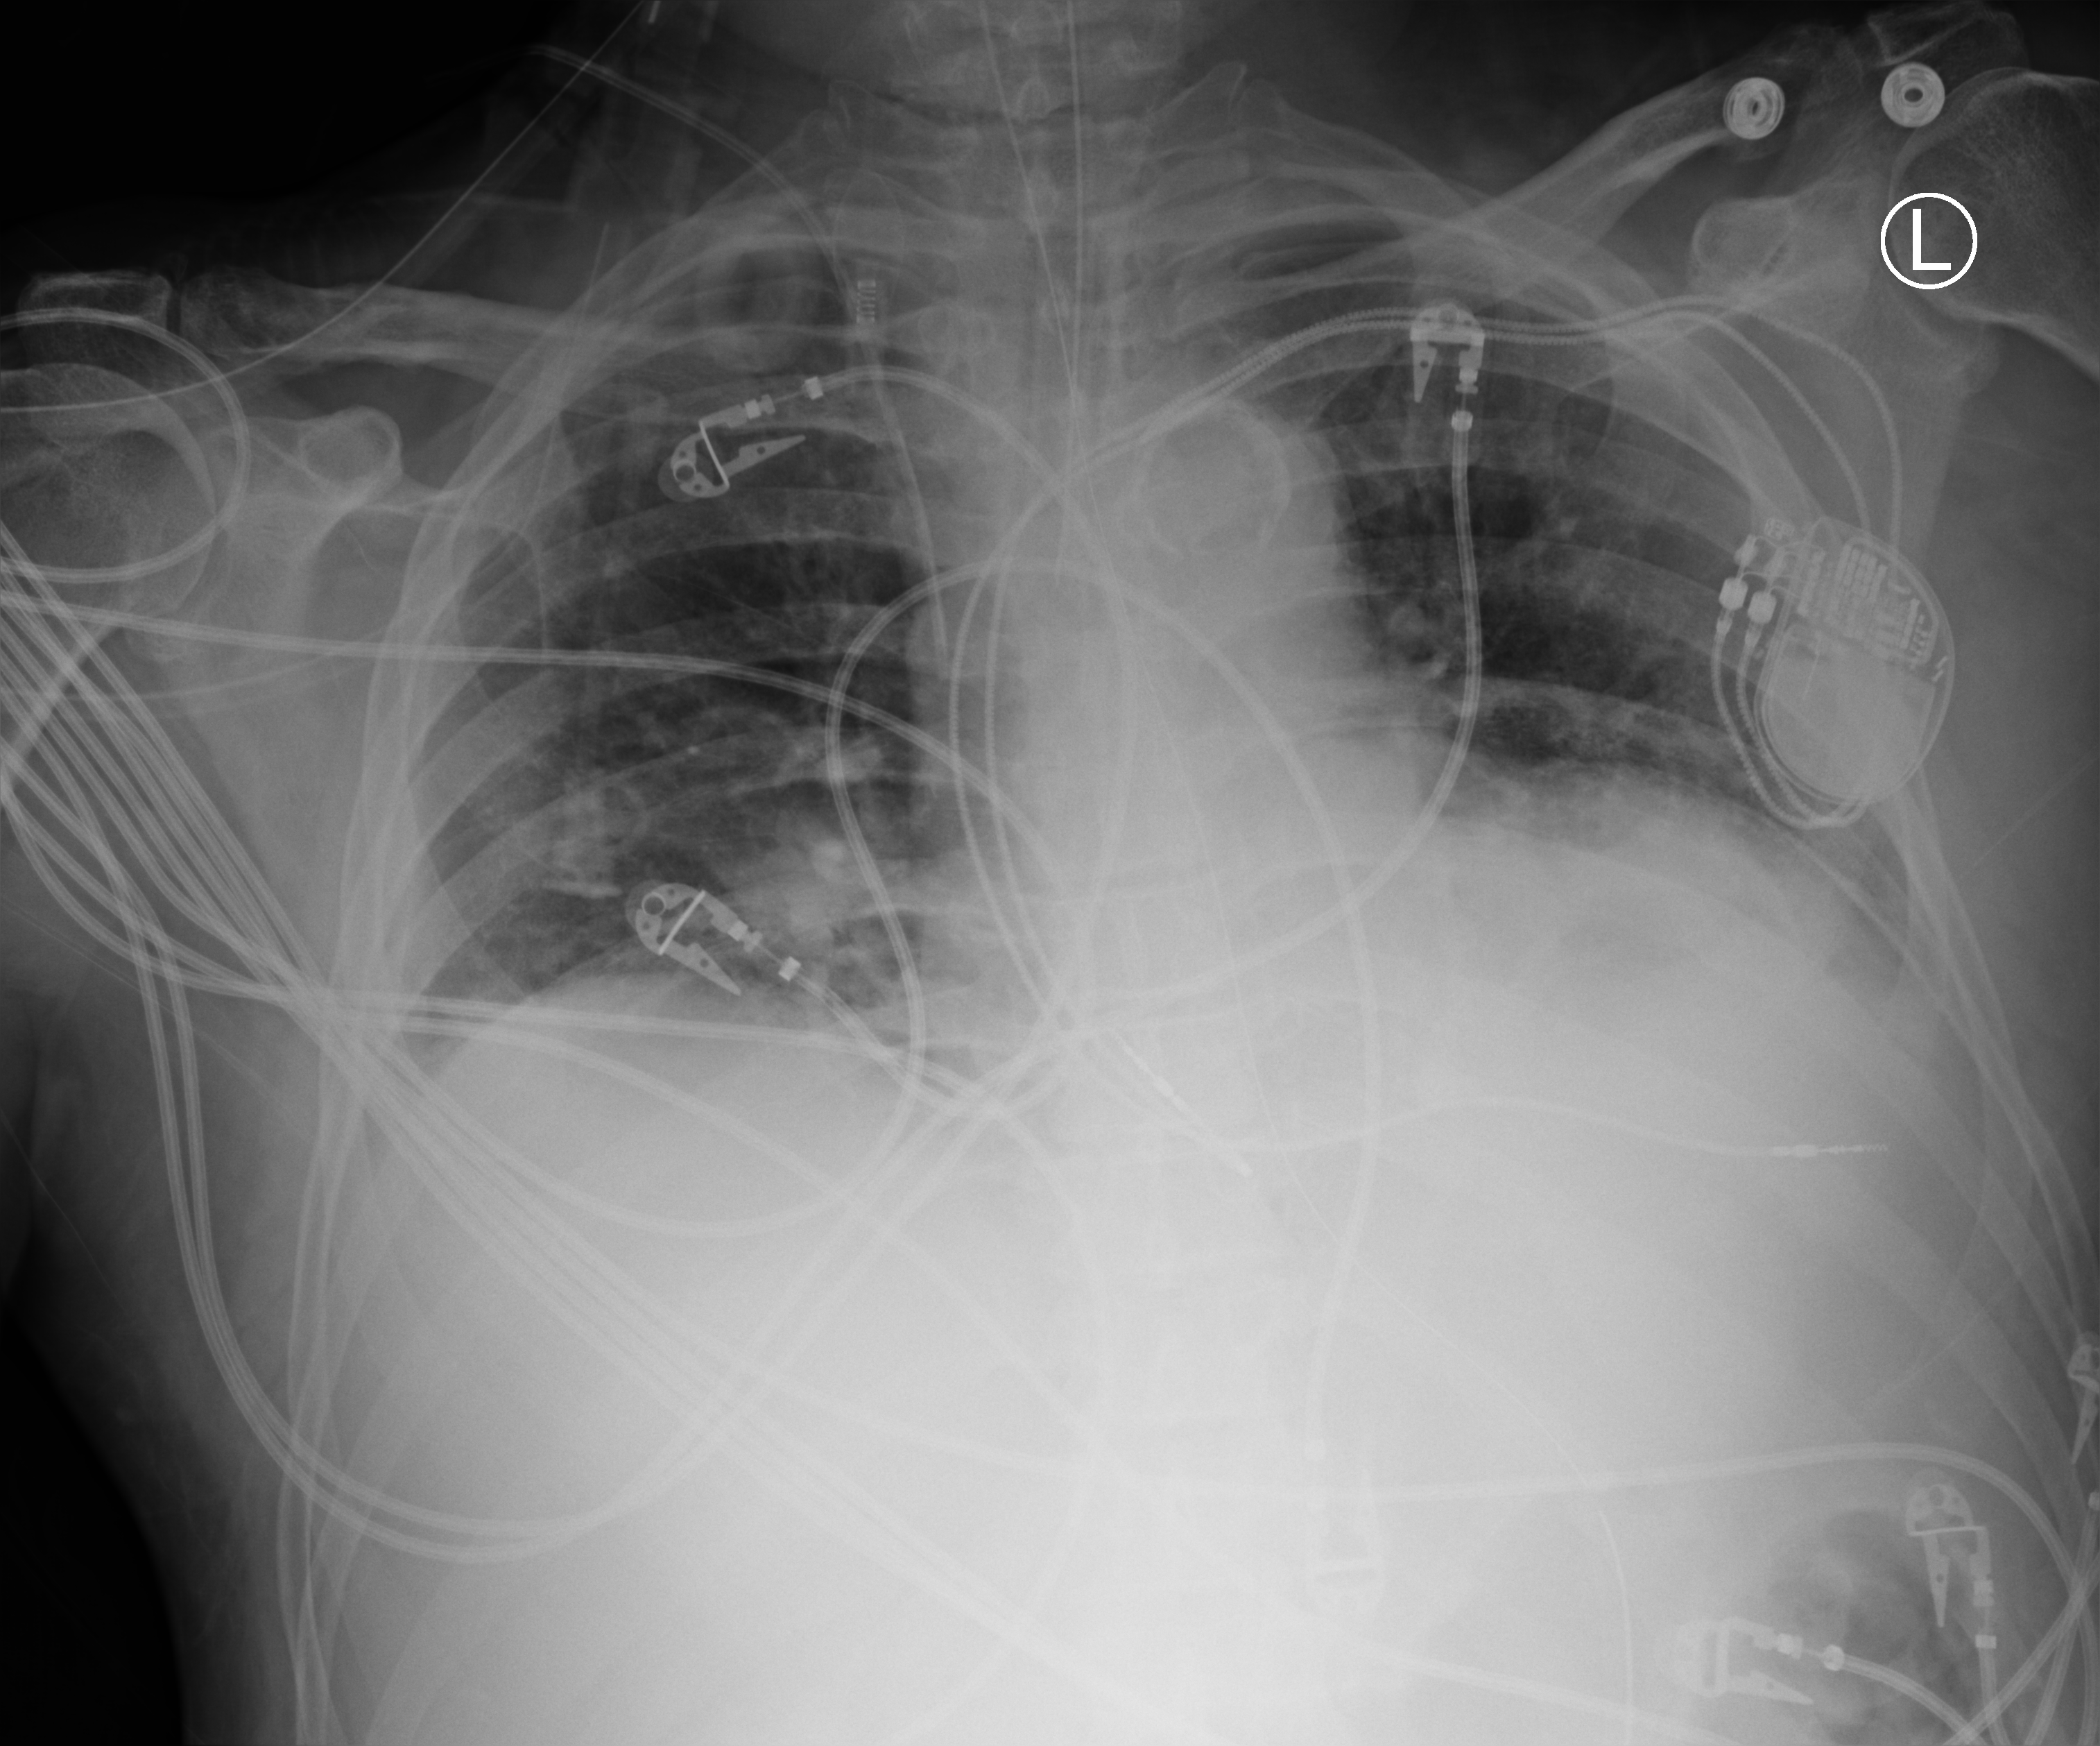
Chest X-ray (portable), anteroposterior (AP) projection. Male patient hospitalised with COVID-19, age 60–74 years.
Hospital-stay facts (about this admission, not read from this image; timing relative to this image not recorded): admitted to intensive care during this hospital stay: yes; length of hospital stay: 41 days; mechanically ventilated during this hospital stay: yes.